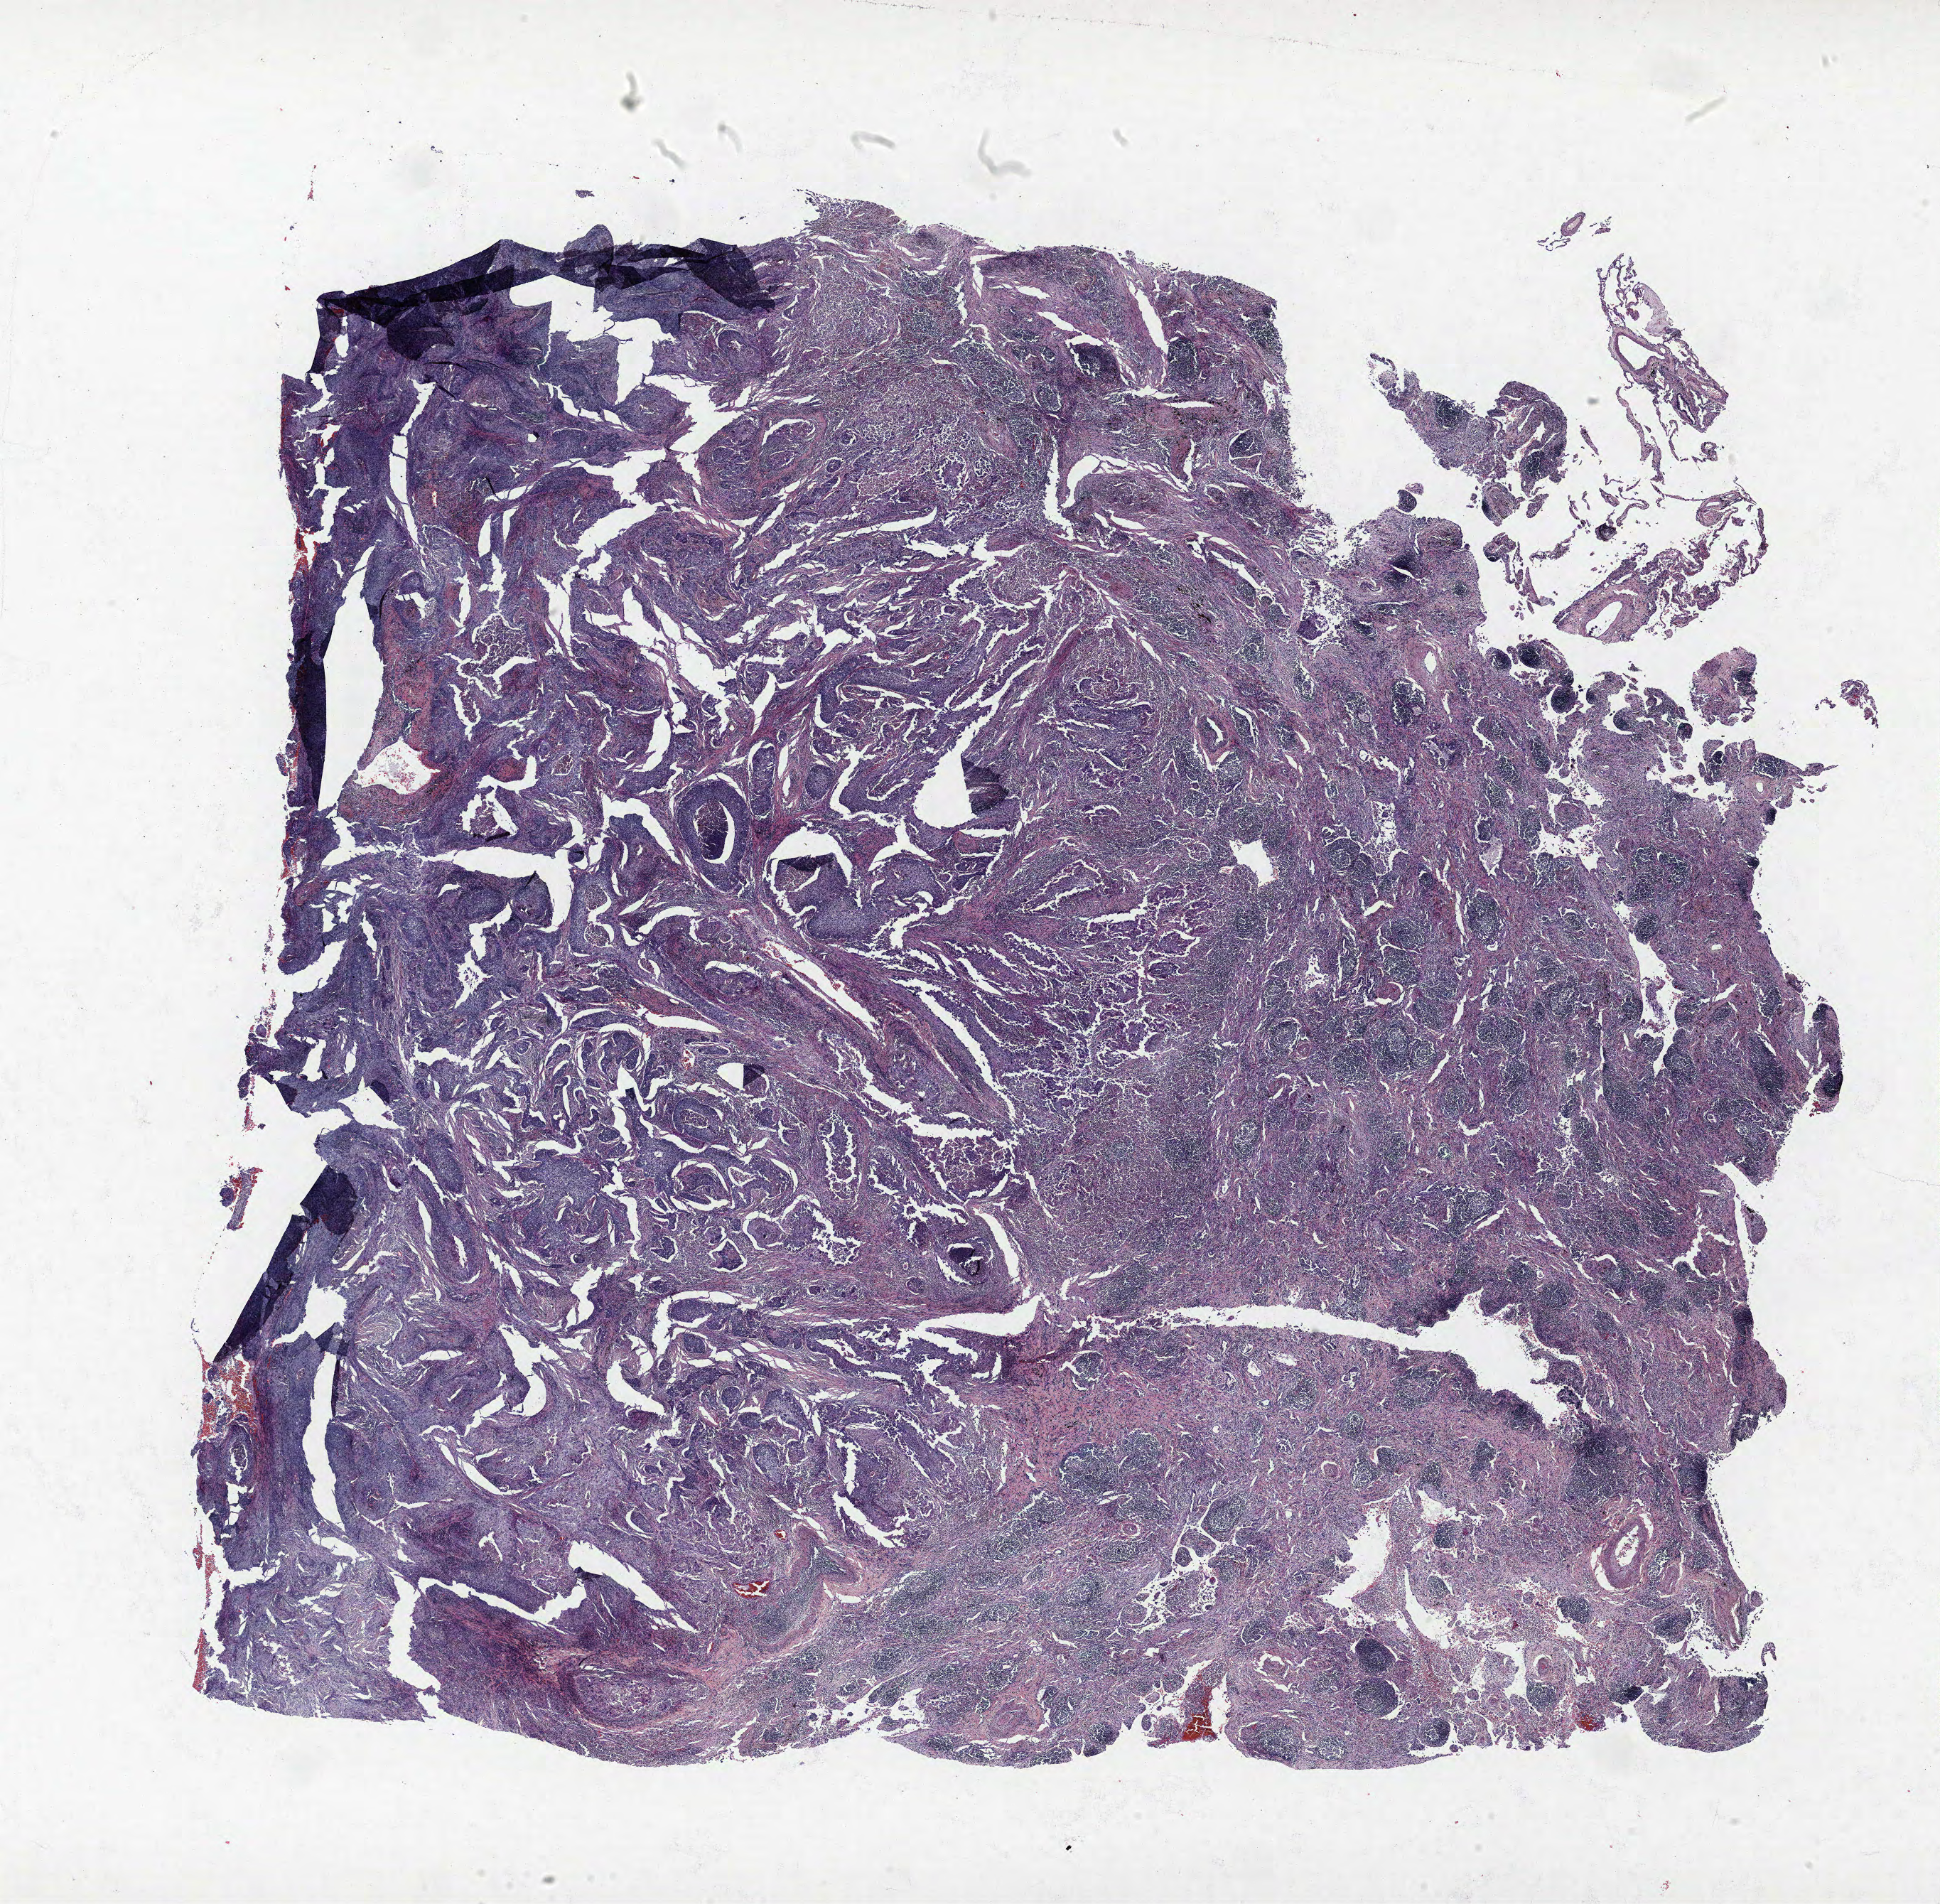
H&E whole-slide image, low-resolution overview of the scanned area, about 21.8 x 21.4 mm. FFPE section. Lung. Male, age 72 at enrolment. Grade: poorly differentiated (G3).
• tumour size (pathology): 43 mm
• participant's lung-cancer diagnosis: Squamous cell carcinoma, NOS
• primary tumour location (clinical record): right upper lobe
• stage (AJCC 6th edition): IIB